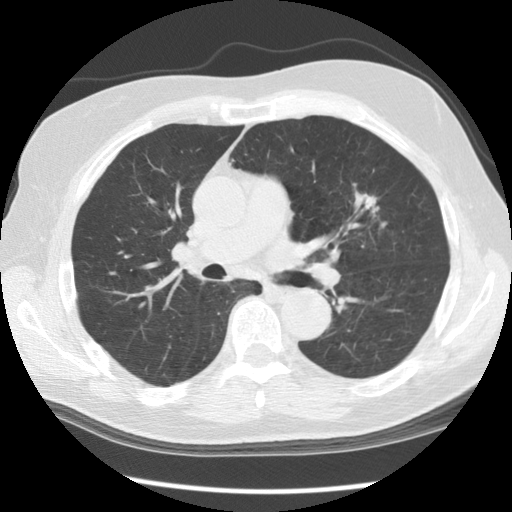
Axial slice from a low-dose chest CT screening exam; second screening round (one year after baseline); lung window (W 1500 / L -600 HU); 2.5 mm slice thickness; standard (soft-tissue) reconstruction kernel (STANDARD); slice 81 of 140 in the series. Male participant, aged 70 years at enrolment.
Expert reader's lesion annotation, box from (x=339, y=178) to (x=398, y=233) px. The screening reader recorded 3 non-calcified nodules or masses ≥4 mm on this exam; which of them this box marks is not recorded. Official screen result: positive, other. Participant outcome: lung cancer diagnosed 396 days after this screen — adenocarcinoma, NOS, left upper lobe, moderately differentiated (G2), stage IIIA (AJCC 6th edition), 17 mm at pathology.